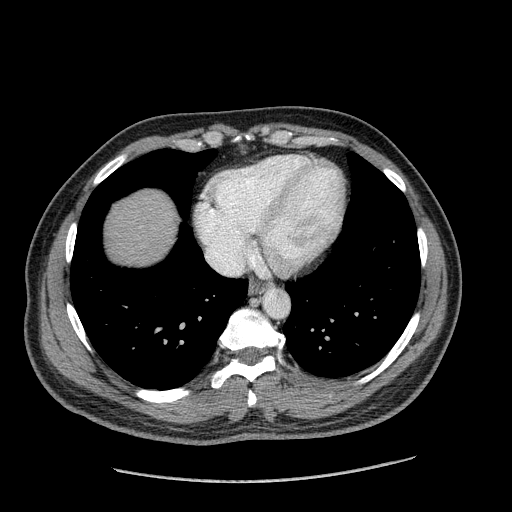
Contrast-enhanced abdominal CT (liver protocol), one axial slice; reconstruction kernel STANDARD; soft-tissue window (W 400 / L 40 HU); 512 × 512 image matrix, field of view 400 × 400 mm. From the clinical record (not read from this slice): diagnosis: hepatocellular carcinoma (patient treated with transarterial chemoembolisation; whether this scan precedes or follows treatment is not stated here); TNM stage (as recorded): Stage-I; Child-Pugh class: A; tumour differentiation: well differentiated; tumour nodularity: uninodular.
Structures marked on this image (semi-automatic segmentation, software-assisted and operator-edited):
- abdominal aorta: bounding box (x1, y1, x2, y2) in pixels: (263, 289, 289, 318)
- liver parenchyma outside the tumour (the mass and vessels are separate outlines, so this box may not span the whole liver): (106, 190, 176, 264)